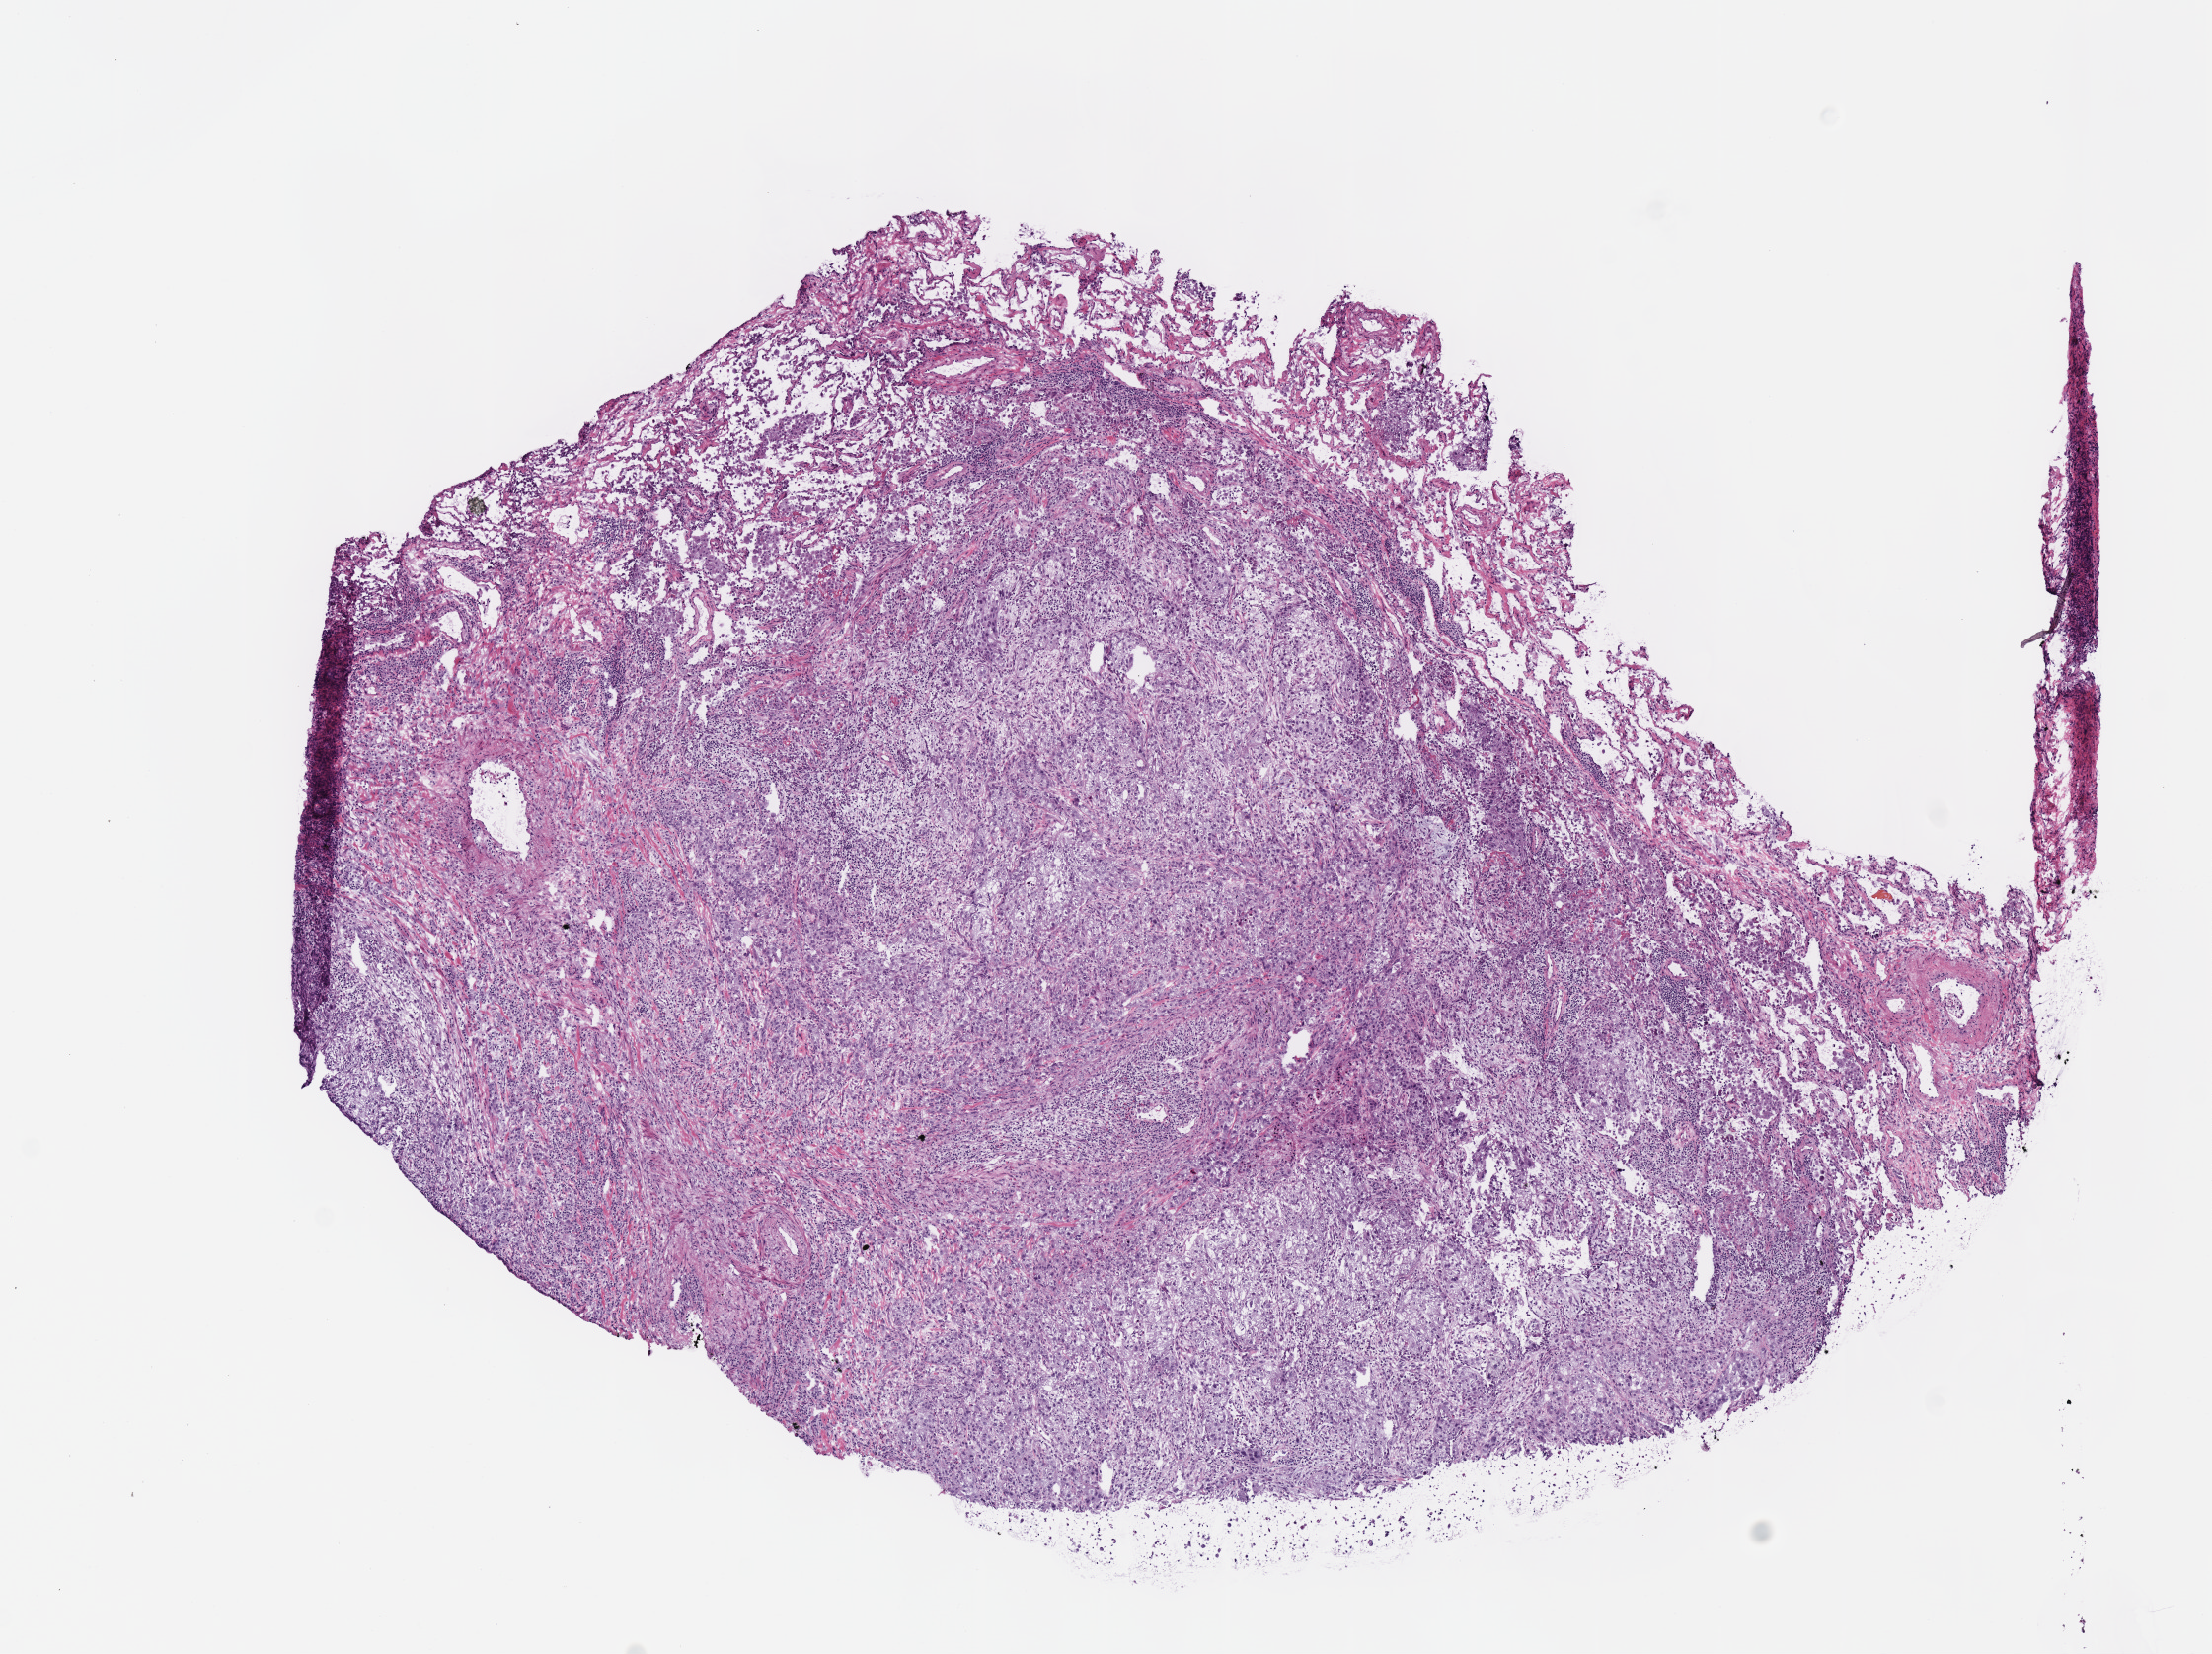
Digitized H&E tissue section (whole slide), low-resolution overview of the scanned area, about 8.8 x 6.6 mm (acquisition: 40x scan), frozen section from the top of the tissue portion, lung, primary tumour sample. Female, age 69 years at initial diagnosis. Pathologist review of this section (percent, as recorded): tumour cells 78%, tumour nuclei 65%, normal cells 15%, stromal cells 5%, necrosis 2%.
* pathologic diagnosis: Adenocarcinoma, NOS (lower lobe, lung)
* AJCC pathologic stage: IB (7th edition)